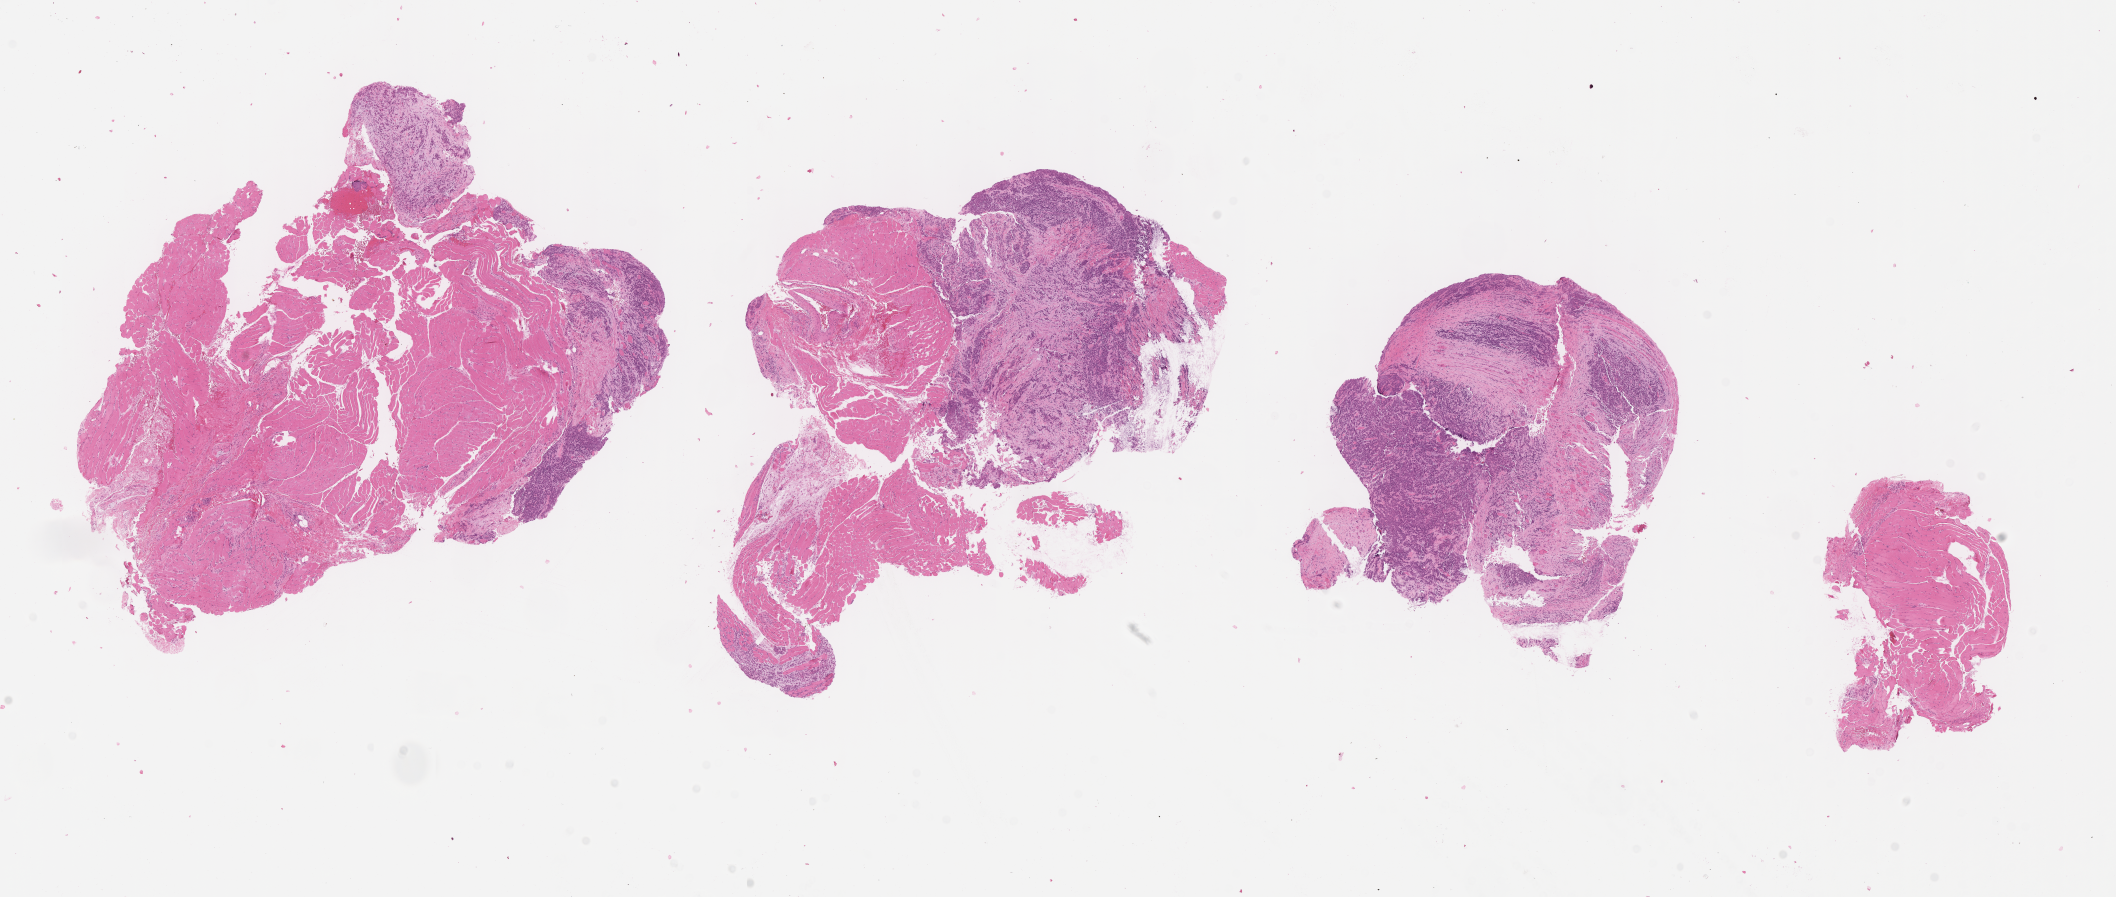
Whole-slide image, hematoxylin and eosin (H&E) stain of tumor tissue — shown as a low-resolution overview of the whole scanned area (about 17.1 x 7.3 mm). FFPE section. Sample anatomic site: soft tissue, foot-left. Patient: female, age 9.3 years at diagnosis.
Diagnosis: rhabdomyosarcoma; histological classification: alveolar rhabdomyosarcoma.